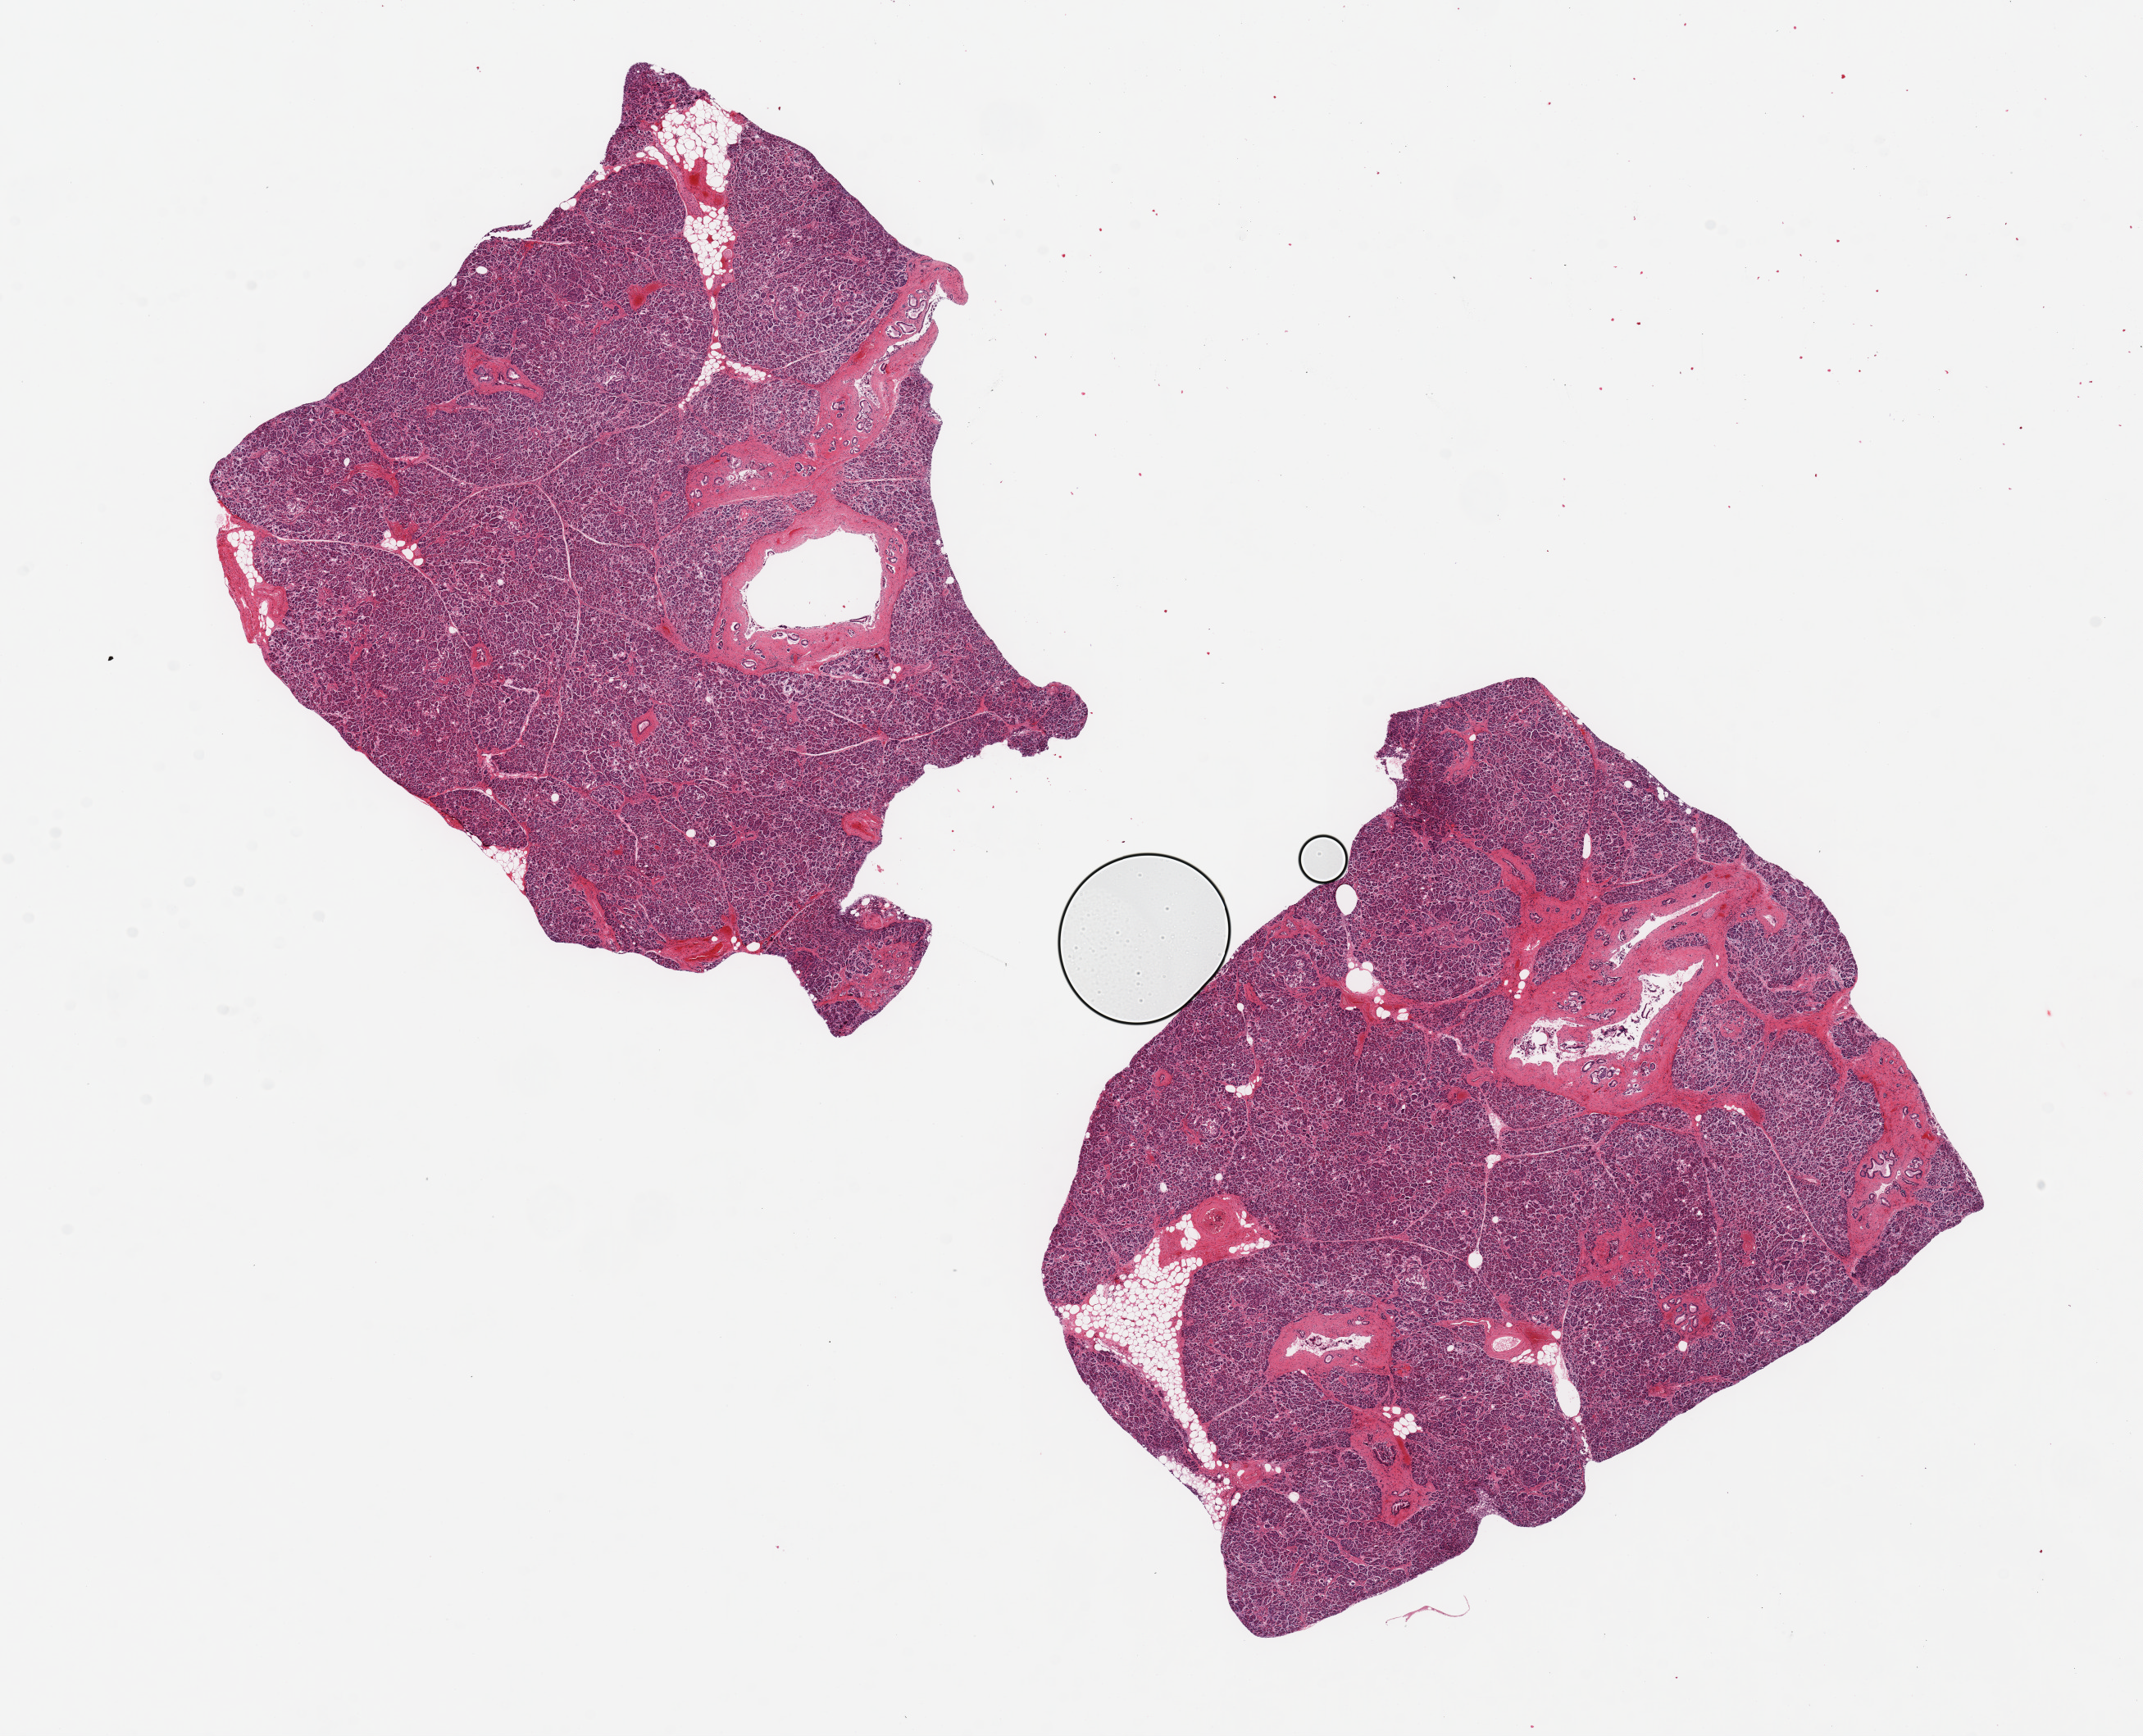
Digitized H&E-stained section, shown as a low-resolution overview of the whole scanned area (about 20.7 x 16.8 mm, slide scanned at 20x). PAXgene-fixed, paraffin-embedded tissue. Sampled site (target tissue): pancreas. Donor tissue sample. Donor: male.
Pathologist's review note for this sample: 2 pieces, 8x6 & 8.5x7mm; patchy interstitial fibrosis; <10% adipose within parenchyma.